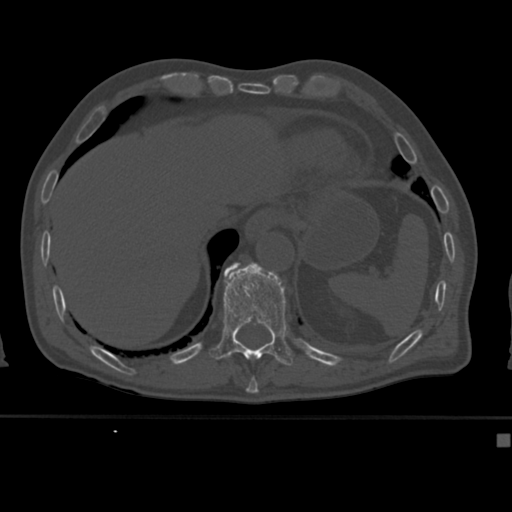
CT including the spine, one axial slice. Slice 212 of 430 in the series (ordered by position). Reconstruction kernel Br40s. 120 kVp. Bone window (W 1800 / L 400 HU). 1.5 mm slice thickness. 512 × 512 image matrix. Patient: male, 64 years. Case-level facts recorded for this patient, not image findings: primary cancer: uterus.
Annotated regions visible in this slice (semi-automatic segmentation, software-assisted and operator-edited):
- T10 vertebra: box from (x=251, y=376) to (x=256, y=382) px
- T11 vertebra: (x=208, y=264)–(x=293, y=366)
- T12 vertebra: (x=226, y=265)–(x=237, y=271)